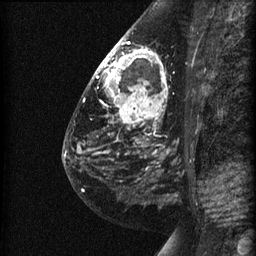
Breast MRI (dynamic contrast-enhanced), one sagittal slice; slice 31 of 60 in the series (ordered by position); dynamic contrast-enhanced series, image 2 of 3 at this slice position (ordered by acquisition); 1.5 T; TE 4.2 ms, TR 22.7 ms; 1.5 mm slice thickness; 256 × 256 image matrix, field of view 180 × 180 mm. Patient: female, 48 years. Case-level facts recorded for this patient, not image findings: setting: breast cancer imaged before/during neoadjuvant chemotherapy; receptor status: triple-negative.
Structures marked on this image (semi-automatically segmented with operator editing):
- analysis volume of interest (the breast-tissue region the enhancement analysis was run in; not a lesion): bounding box [x1, y1, x2, y2] px = [89, 27, 191, 180]
- tumour enhancement mask (voxels above the 90 % enhancement threshold inside the analysis volume of interest): [95, 39, 164, 114]